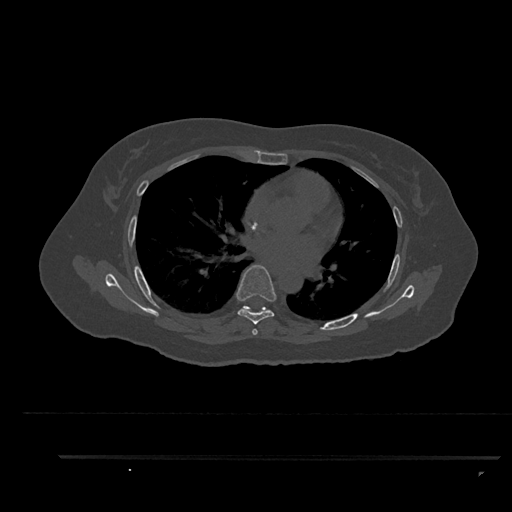
CT including the spine, one axial slice; slice 552 of 797 in the series (ordered by position); 120 kVp; bone window (W 1800 / L 400 HU); 512 × 512 image matrix. Female patient, age 44 years. Case-level facts recorded for this patient, not image findings: primary cancer: renal.
Outlined on this slice (semi-automatically segmented with operator editing):
- T6 vertebra: bounding box (x1, y1, x2, y2) in pixels: (236, 265, 276, 335)
- T7 vertebra: (250, 308, 252, 312)